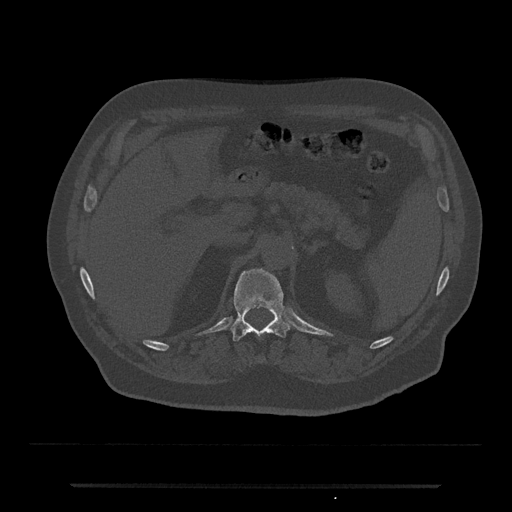
CT including the spine, one axial slice. Slice 597 of 797 in the series (ordered by position). Reconstruction kernel Br40s/3. Bone window (W 1800 / L 400 HU). 0.5 mm slice thickness. 512 × 512 image matrix. Male patient, age 80 years. From the clinical record (not read from this slice): primary cancer: prostate; vertebrae with lytic lesions (as recorded): L1, T11.
Outlined on this slice (semi-automatically segmented with operator editing):
- T12 vertebra: box from (x=230, y=268) to (x=291, y=341) px